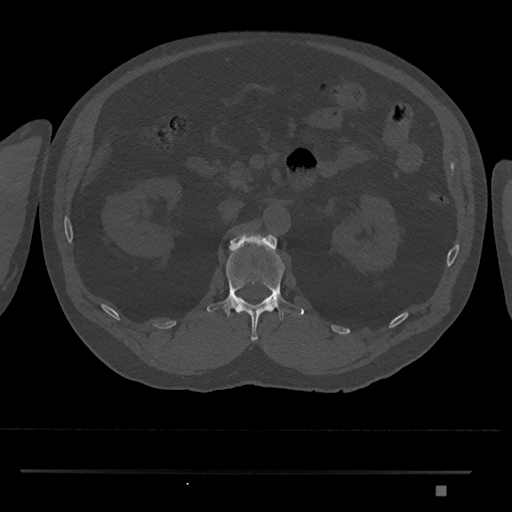
CT including the spine, one axial slice. Slice 817 of 1134 in the series (ordered by position). 120 kVp. Bone window (W 1800 / L 400 HU). 0.5 mm slice thickness. 512 × 512 image matrix, field of view 429 × 429 mm. Male patient, age 65 years. From the clinical record (not read from this slice): primary cancer: prostate.
Outlined on this slice (semi-automatically segmented with operator editing):
- L1 vertebra: bounding box [x1, y1, x2, y2] px = [207, 232, 304, 341]